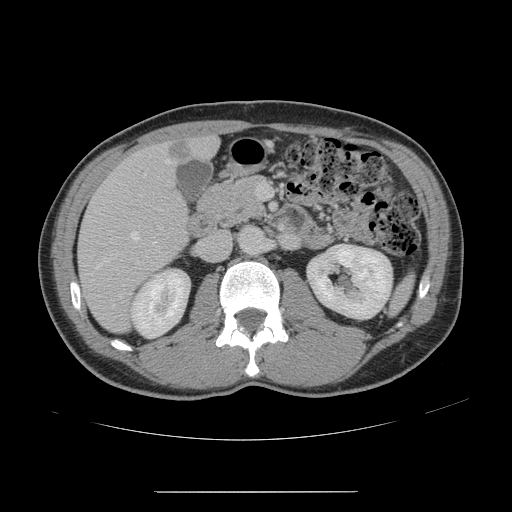
Contrast-enhanced abdominal CT, one axial slice. Slice 68 of 178 in the series (ordered by position). 120 kVp. Intravenous contrast given. Soft-tissue window (W 400 / L 40 HU). 512 × 512 image matrix. Male patient, age 53 years. Case-level facts recorded for this patient, not image findings: diagnosis: colorectal cancer liver metastases, imaged before liver resection; multiple liver metastases: yes.
Annotated regions visible in this slice (outlined manually by an expert reader):
- hepatic veins: bounding box (x1, y1, x2, y2) in pixels: (95, 160, 170, 270)
- liver: (79, 138, 217, 332)
- planned liver remnant (the part of the liver to remain after resection): (196, 137, 217, 158)
- portal vein (with intrahepatic branches): (140, 184, 267, 199)
- liver metastasis: (169, 141, 190, 159)